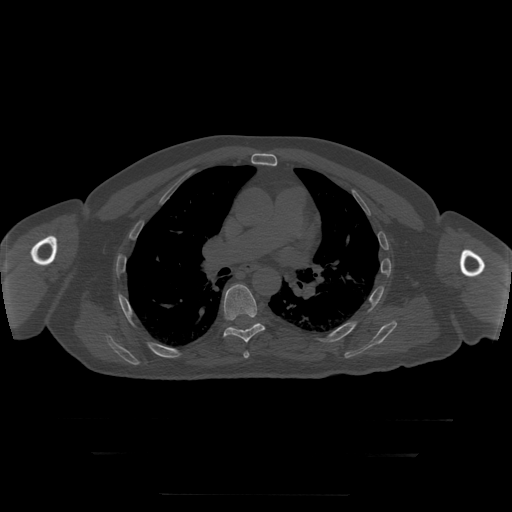
CT including the spine, one axial slice. Position 187 of 397 along the scan axis. 120 kVp. Bone window (W 1800 / L 400 HU). 512 × 512 image matrix, field of view 510 × 510 mm. Patient age 73 years. From the clinical record (not read from this slice): primary cancer: prostate.
Structures marked on this image (semi-automatically segmented with operator editing):
- T6 vertebra: bounding box <244,352,250,359> (left, top, right, bottom; pixels)
- T7 vertebra: <224,284,265,343>
- T8 vertebra: <230,327,252,330>